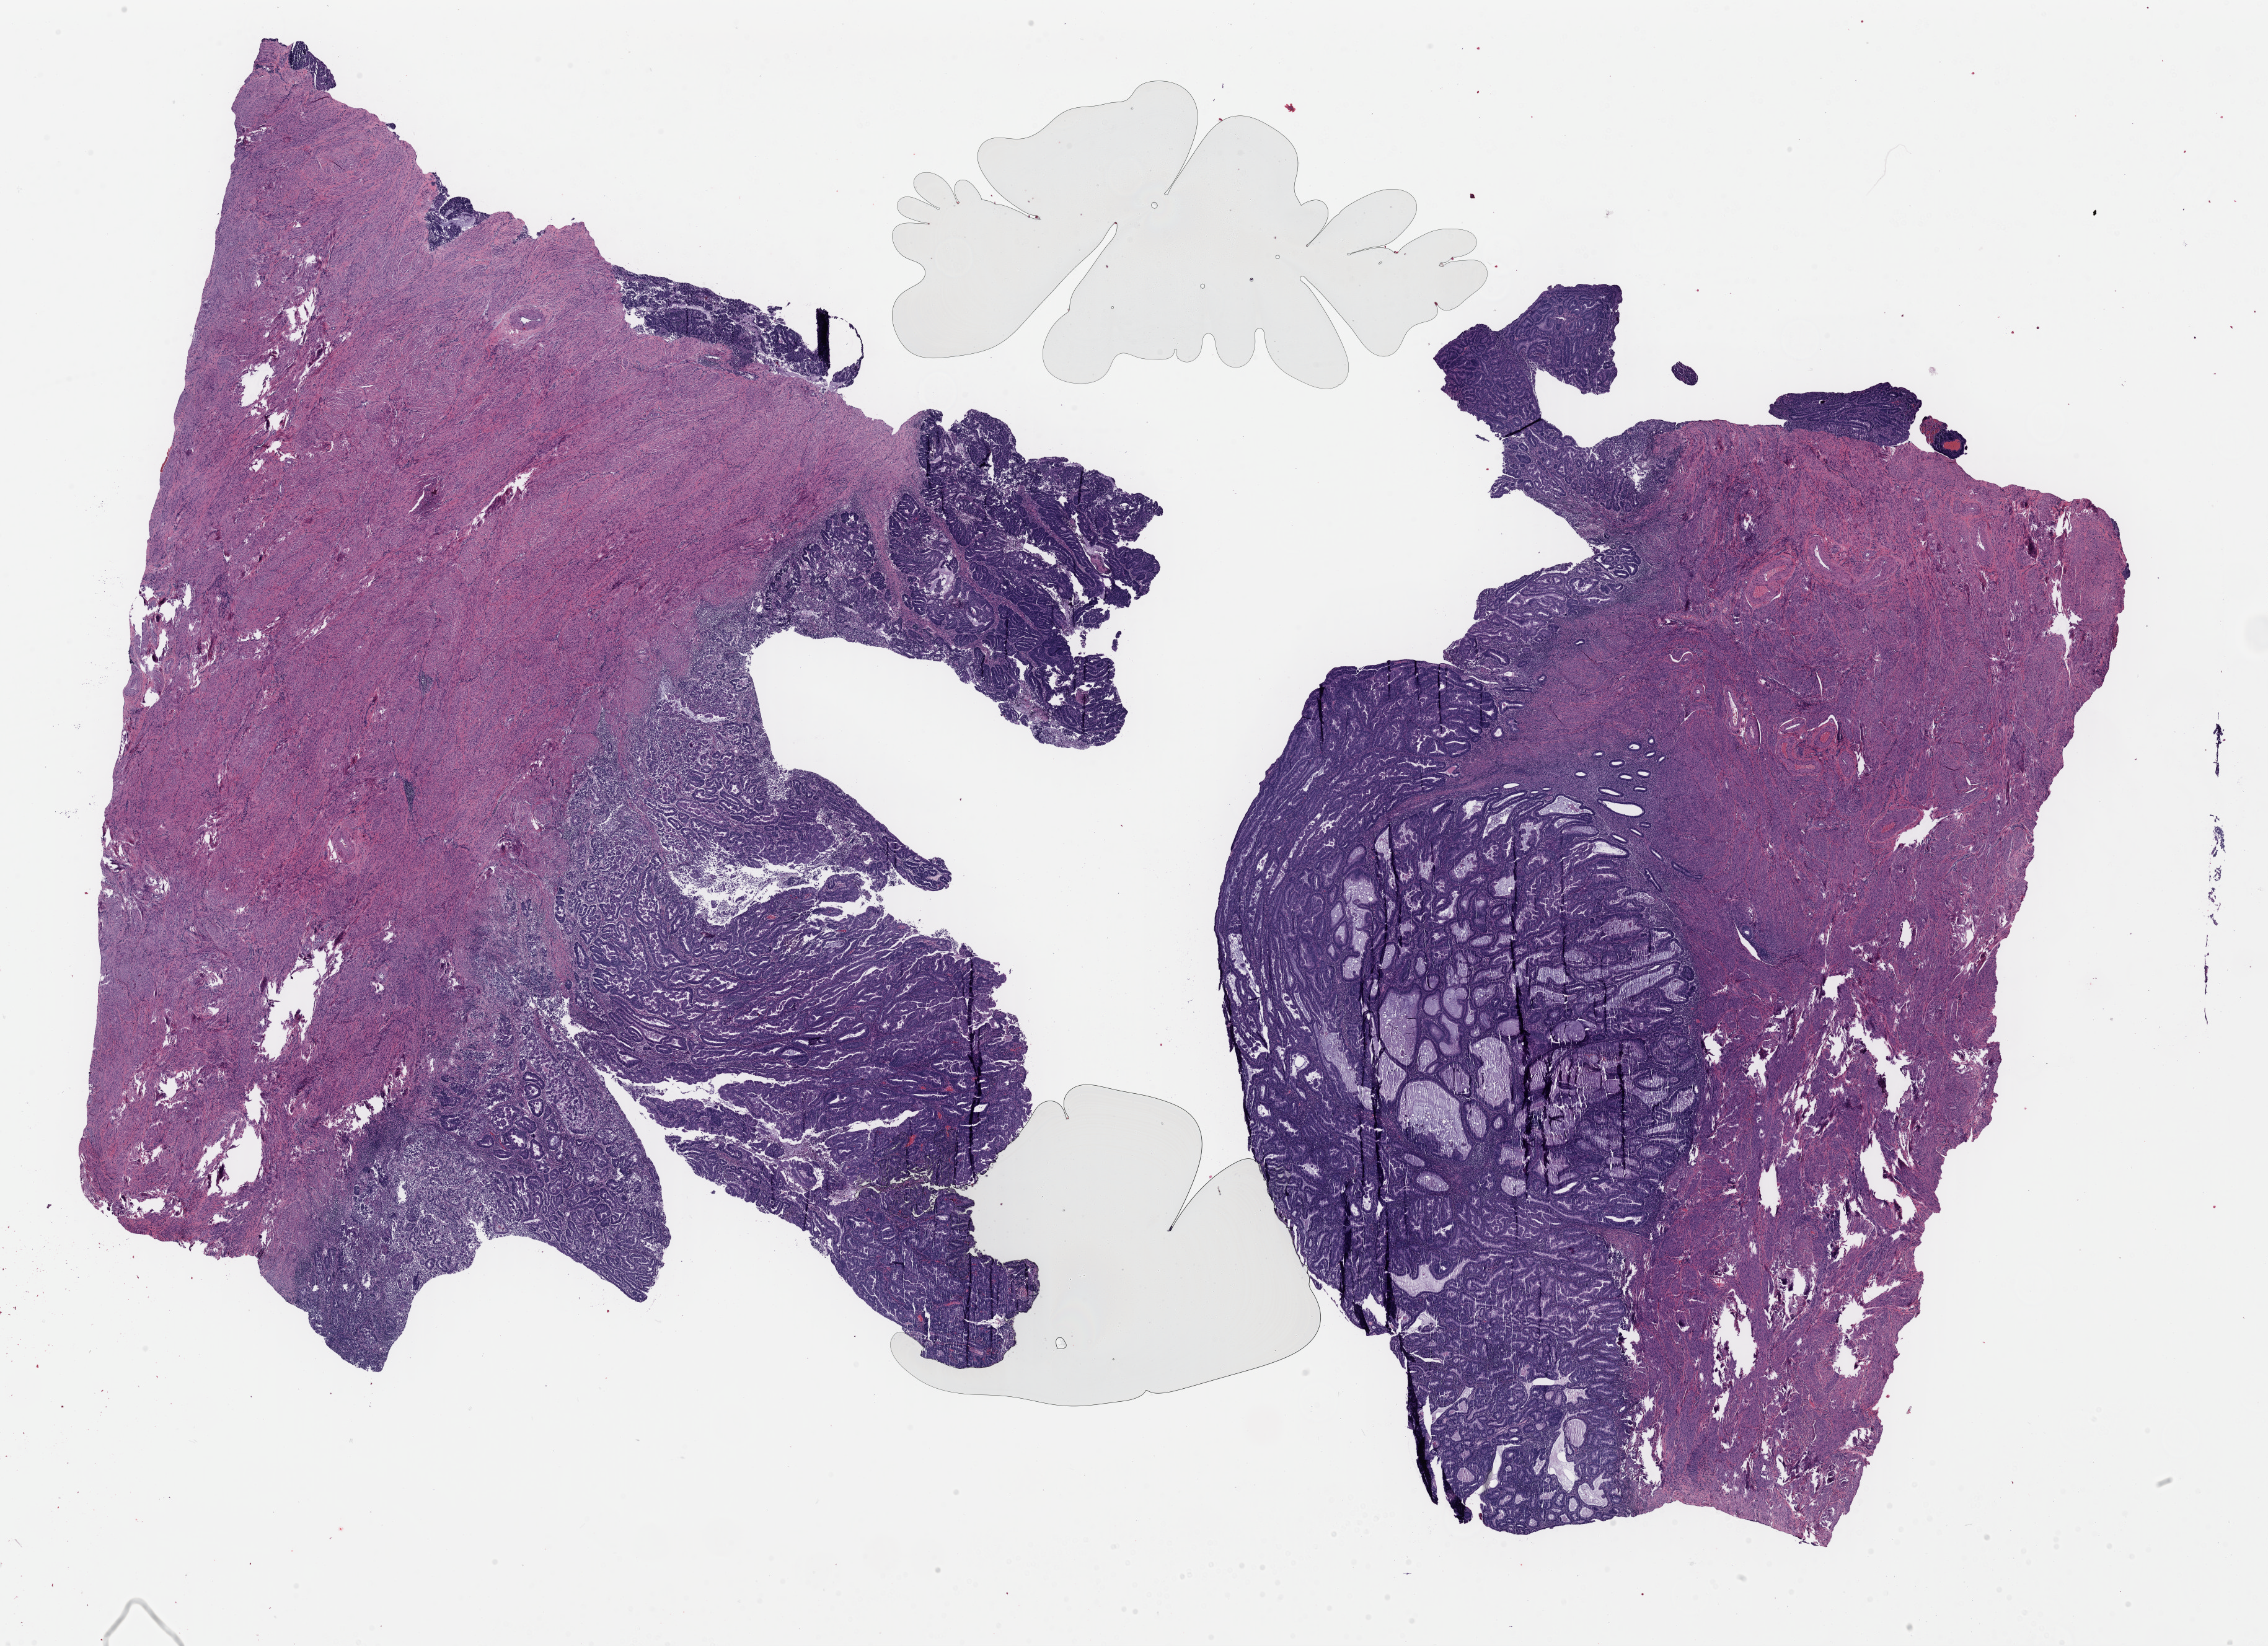
Whole-slide histology image, Hematoxylin and eosin (H&E) stained — whole scanned area (about 28.9 x 21.0 mm, acquisition: 40x scan) shown as a low-resolution overview, FFPE section, sample: primary tumour, uterus. Female, age 53 years at initial diagnosis. Histologic grade: G2 (moderately differentiated).
* diagnosis: Endometrioid adenocarcinoma, NOS (endometrium)
* FIGO stage: I